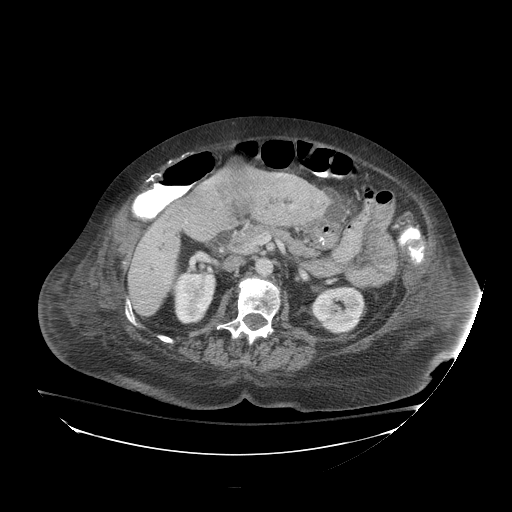
Contrast-enhanced abdominal CT (liver protocol), one axial slice. Slice 32 of 81 in the series (ordered by position). Reconstruction kernel STANDARD. 140 kVp. Soft-tissue window (W 400 / L 40 HU). 512 × 512 image matrix, field of view 500 × 500 mm. From the clinical record (not read from this slice): diagnosis: hepatocellular carcinoma (patient treated with transarterial chemoembolisation; whether this scan precedes or follows treatment is not stated here); TNM stage (as recorded): Stage-I.
Structures marked on this image (semi-automatic segmentation, software-assisted and operator-edited):
- liver parenchyma outside the tumour (the mass and vessels are separate outlines, so this box may not span the whole liver): bounding box (x1, y1, x2, y2) in pixels: (120, 170, 298, 316)
- mass: (217, 160, 254, 213)
- liver vessels: (277, 174, 281, 177)